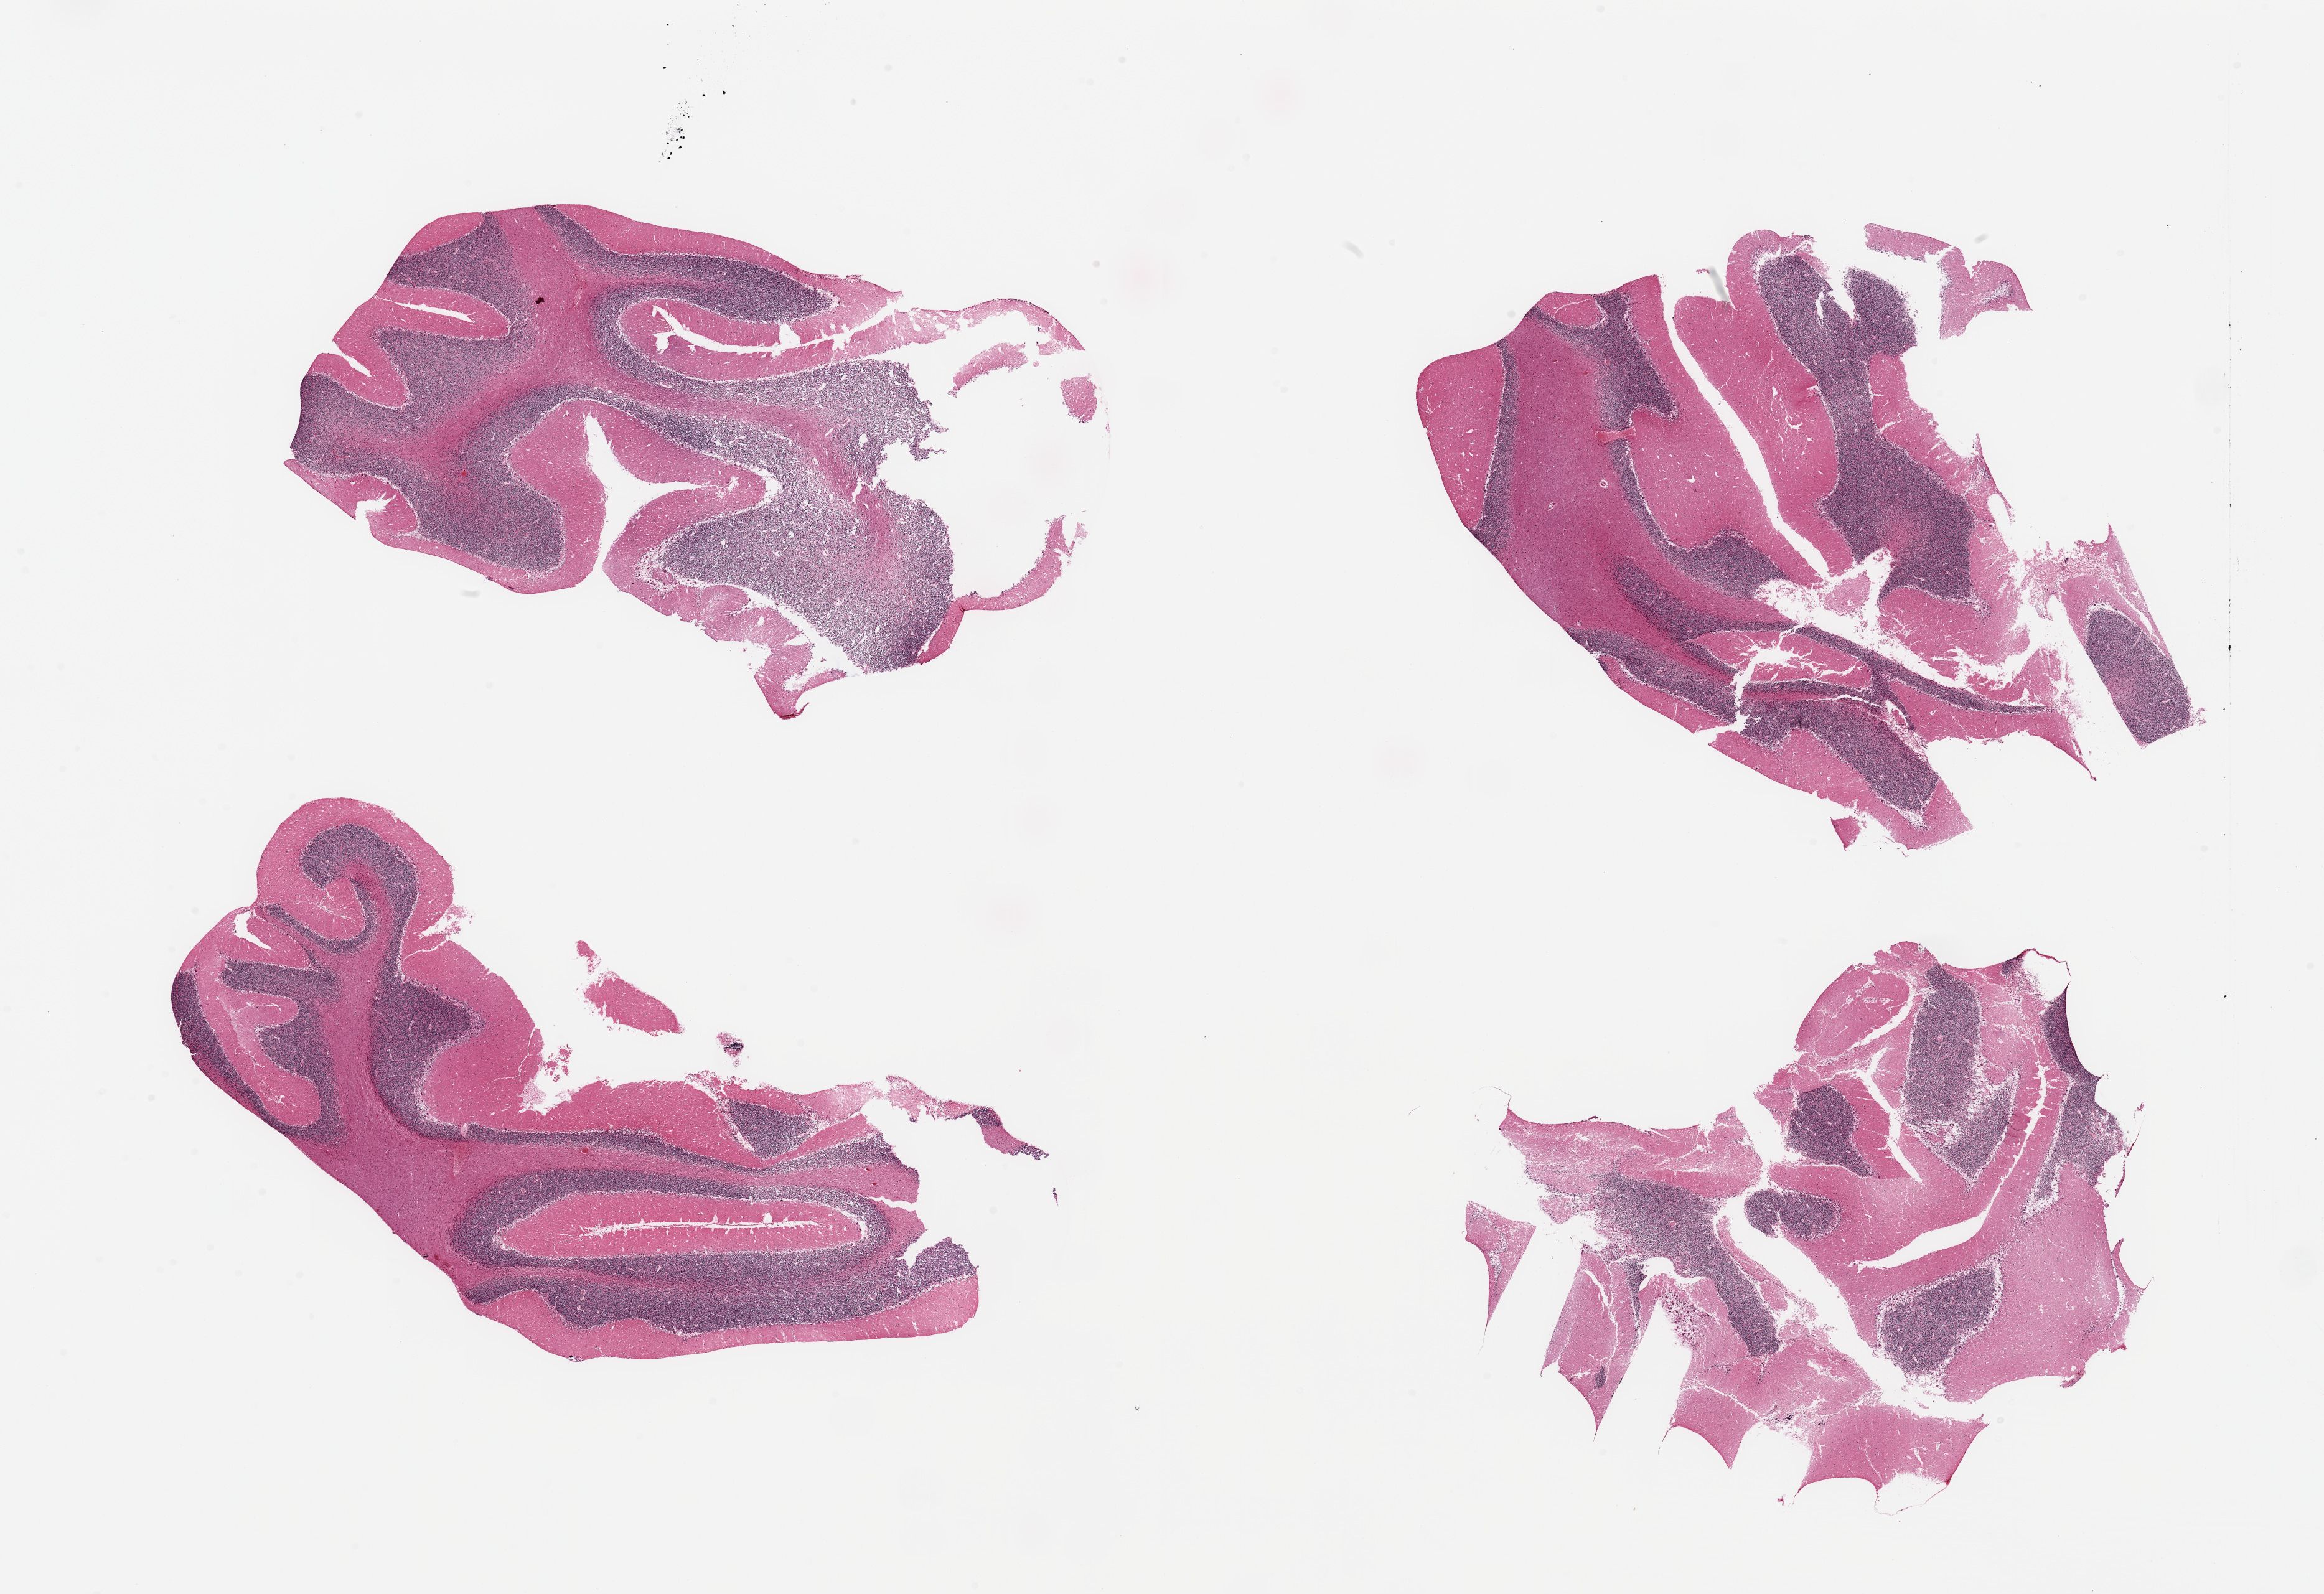
Digitized H&E-stained section, brightfield — a low-resolution overview of the entire scanned area, about 29.5 x 20.3 mm, PAXgene-fixed, paraffin-embedded tissue, section of cerebellum (target tissue), donor tissue sample. Male donor.
Pathologist's review note for this sample: 4 fragmented pieces.